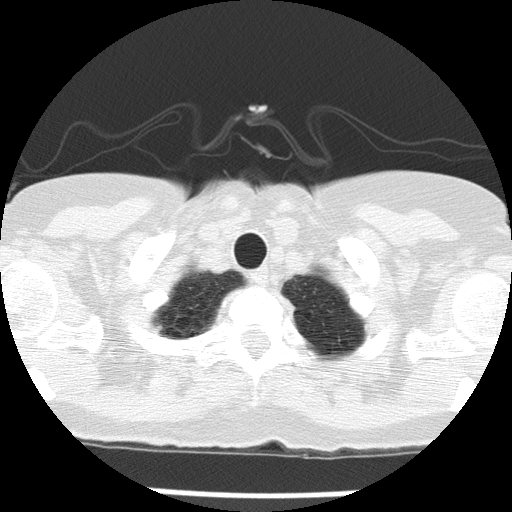
Low-dose screening chest CT, one axial slice; lung window (W 1500 / L -600 HU); 2 mm slice thickness; 512 × 512 image matrix, field of view 276 × 276 mm.
Annotated regions visible in this slice (manually delineated by an expert):
- lesion 1 (tumor, upper lobe of left lung): bounding box (x1, y1, x2, y2) in pixels: (281, 295, 296, 316)